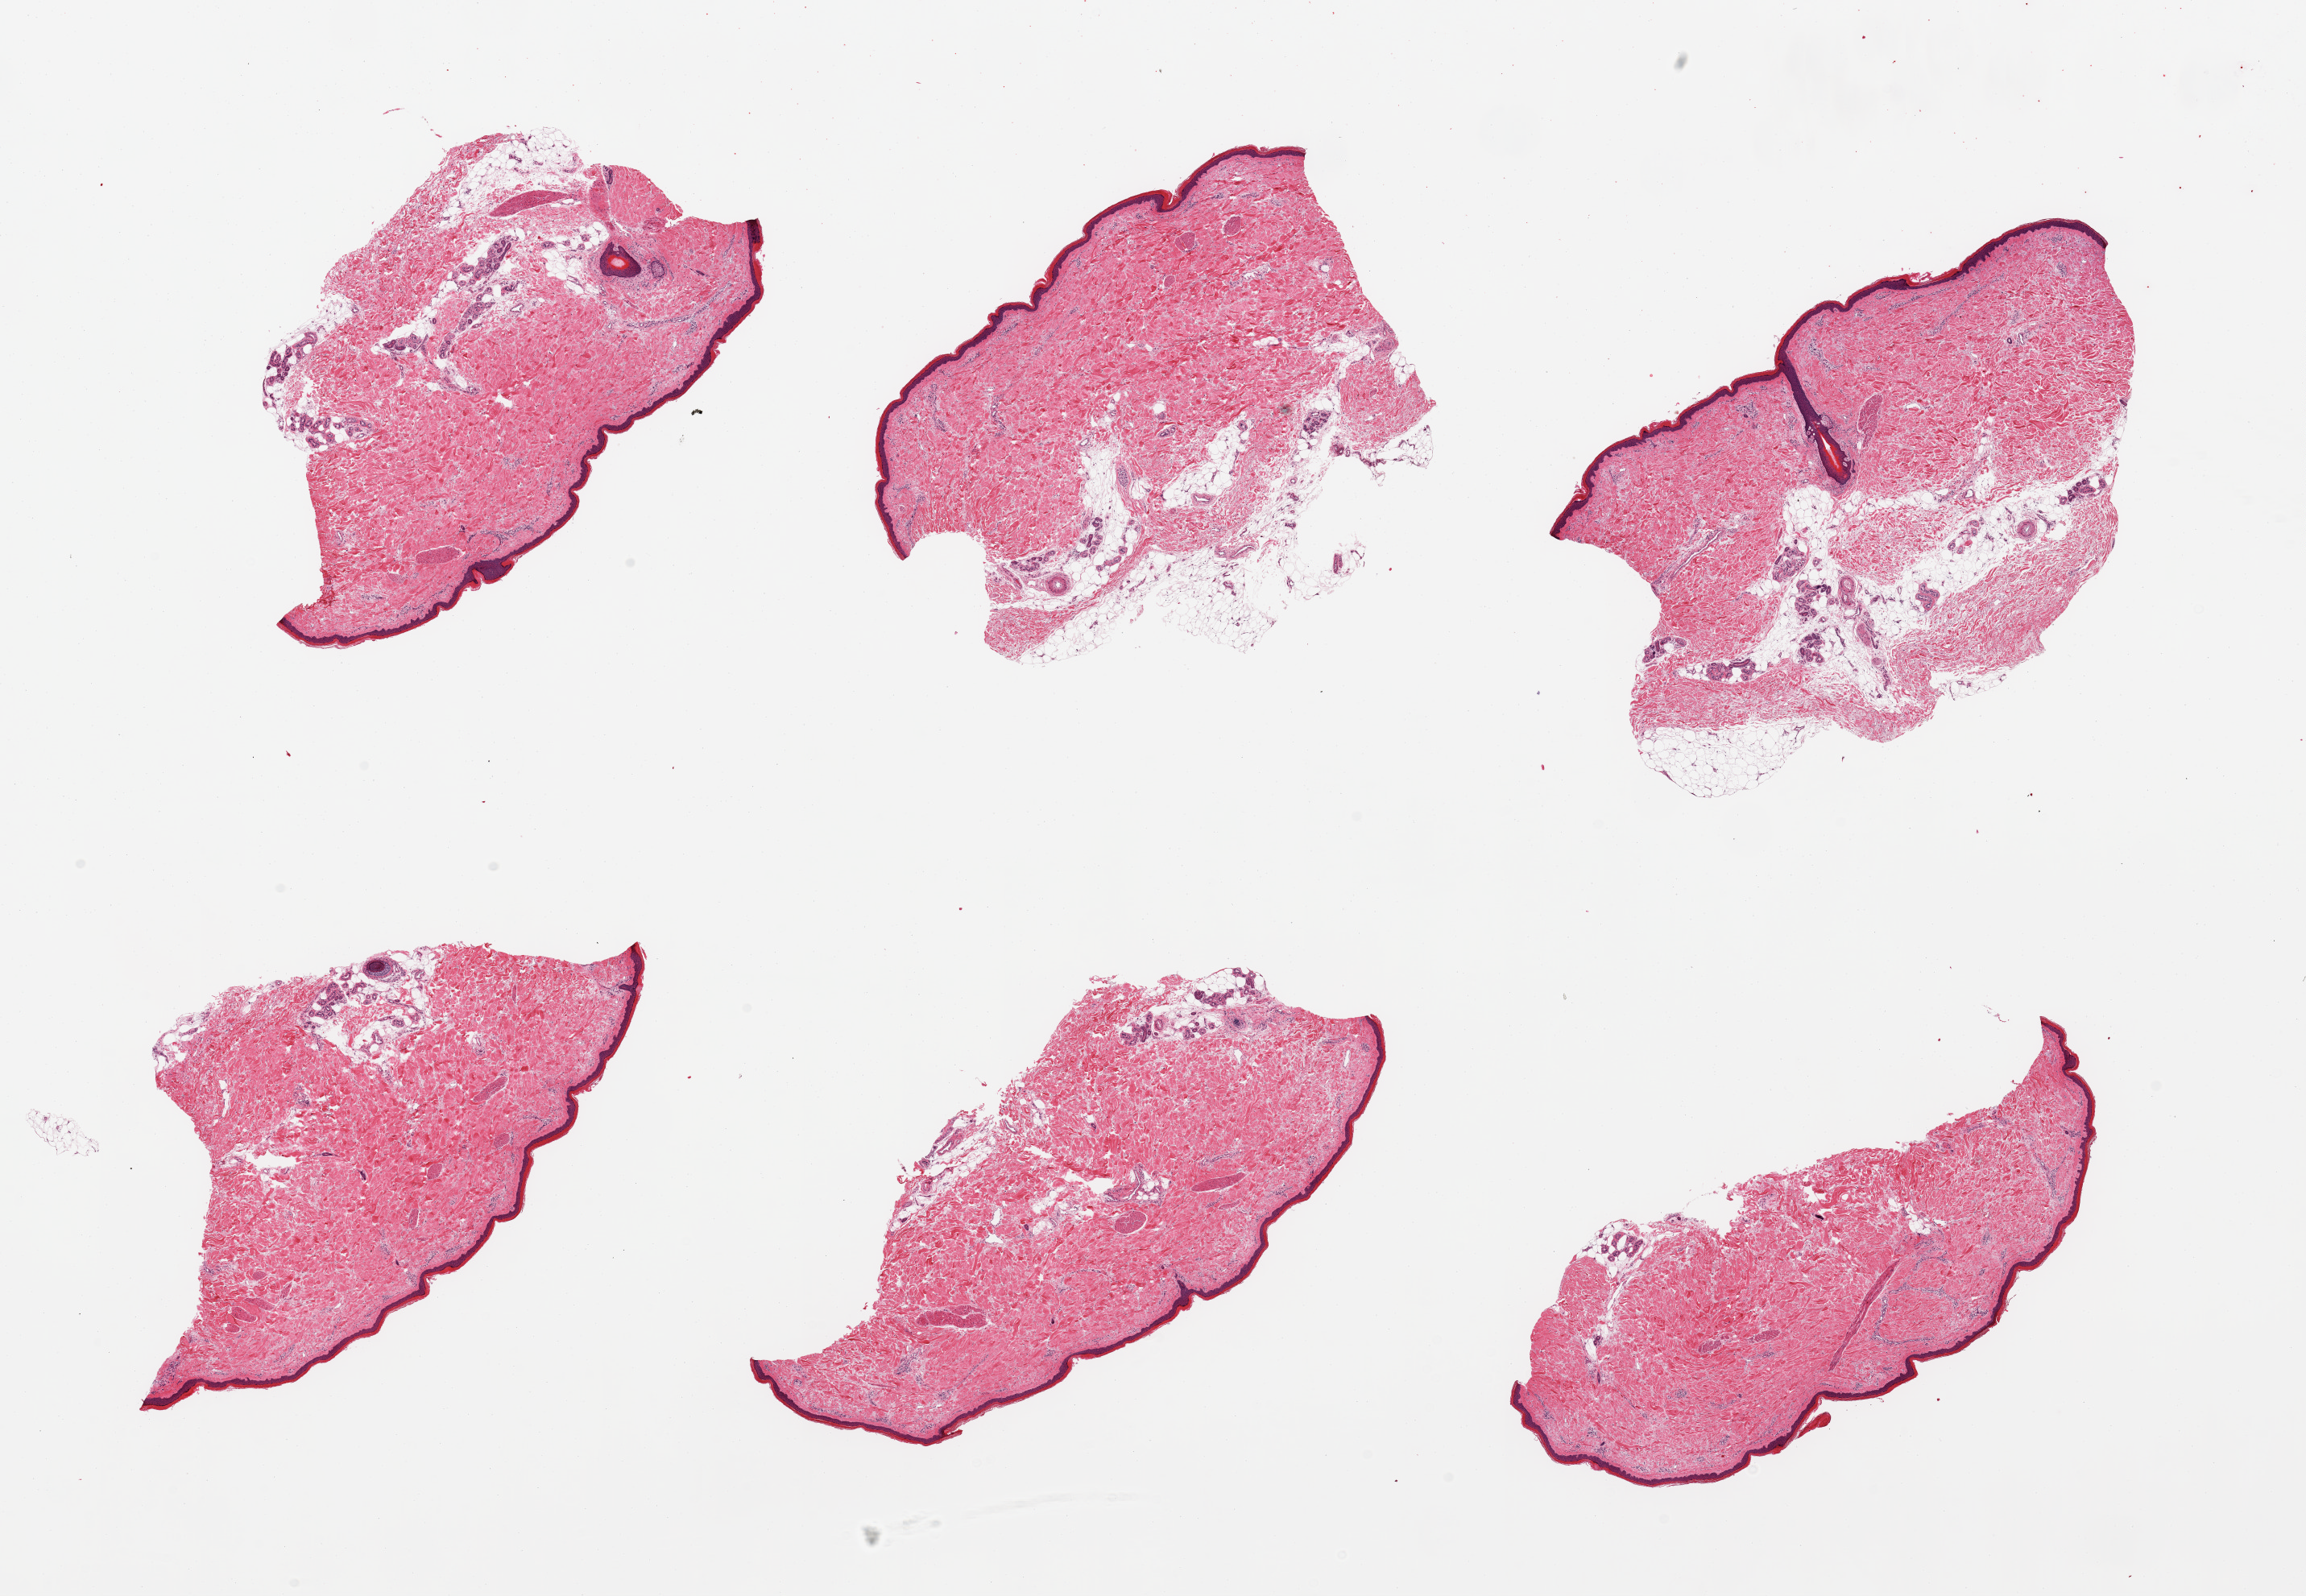
Digitized H&E-stained section, low-resolution overview of the scanned area, about 22.6 x 15.7 mm. PAXgene-fixed, paraffin-embedded tissue. Section of skin of lower leg (target tissue). Donor tissue sample. Donor: male.
- review note (as recorded): 6 pieces, minimal dermal fat, squamous epithelium is ~50 microns